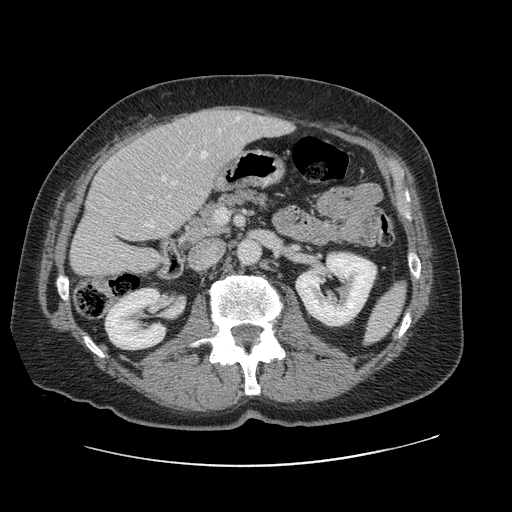
Contrast-enhanced abdominal CT, one axial slice. Position 41 of 138 along the scan axis. Intravenous contrast given. Soft-tissue window (W 400 / L 40 HU). 2.5 mm slice thickness. 512 × 512 image matrix, field of view 402 × 402 mm. Male patient, age 71 years. Case-level facts recorded for this patient, not image findings: diagnosis: colorectal cancer liver metastases, imaged before liver resection; multiple liver metastases: no; largest metastasis: 3.3 cm; disease in both lobes: no.
Outlined on this slice (expert manual segmentation):
- hepatic veins: bounding box [x1, y1, x2, y2] px = [94, 116, 240, 265]
- liver: [72, 107, 291, 277]
- planned liver remnant (the part of the liver to remain after resection): [72, 135, 192, 278]
- portal vein (with intrahepatic branches): [162, 177, 166, 181]